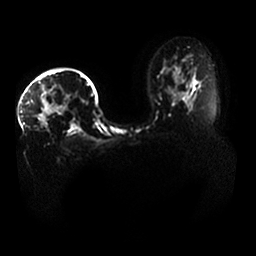
Breast MRI, one axial slice. Slice 26 of 33 in the series (ordered by position). Diffusion-weighted series; image 2 of 4 stored at this slice position (different b-values; order by instance number). 1.5 T. 4 mm slice thickness. 256 × 256 image matrix, field of view 400 × 400 mm. Female patient.
Annotated regions visible in this slice (manually delineated by an expert):
- tumour on diffusion-weighted imaging: bounding box <42,89,78,115> (left, top, right, bottom; pixels)